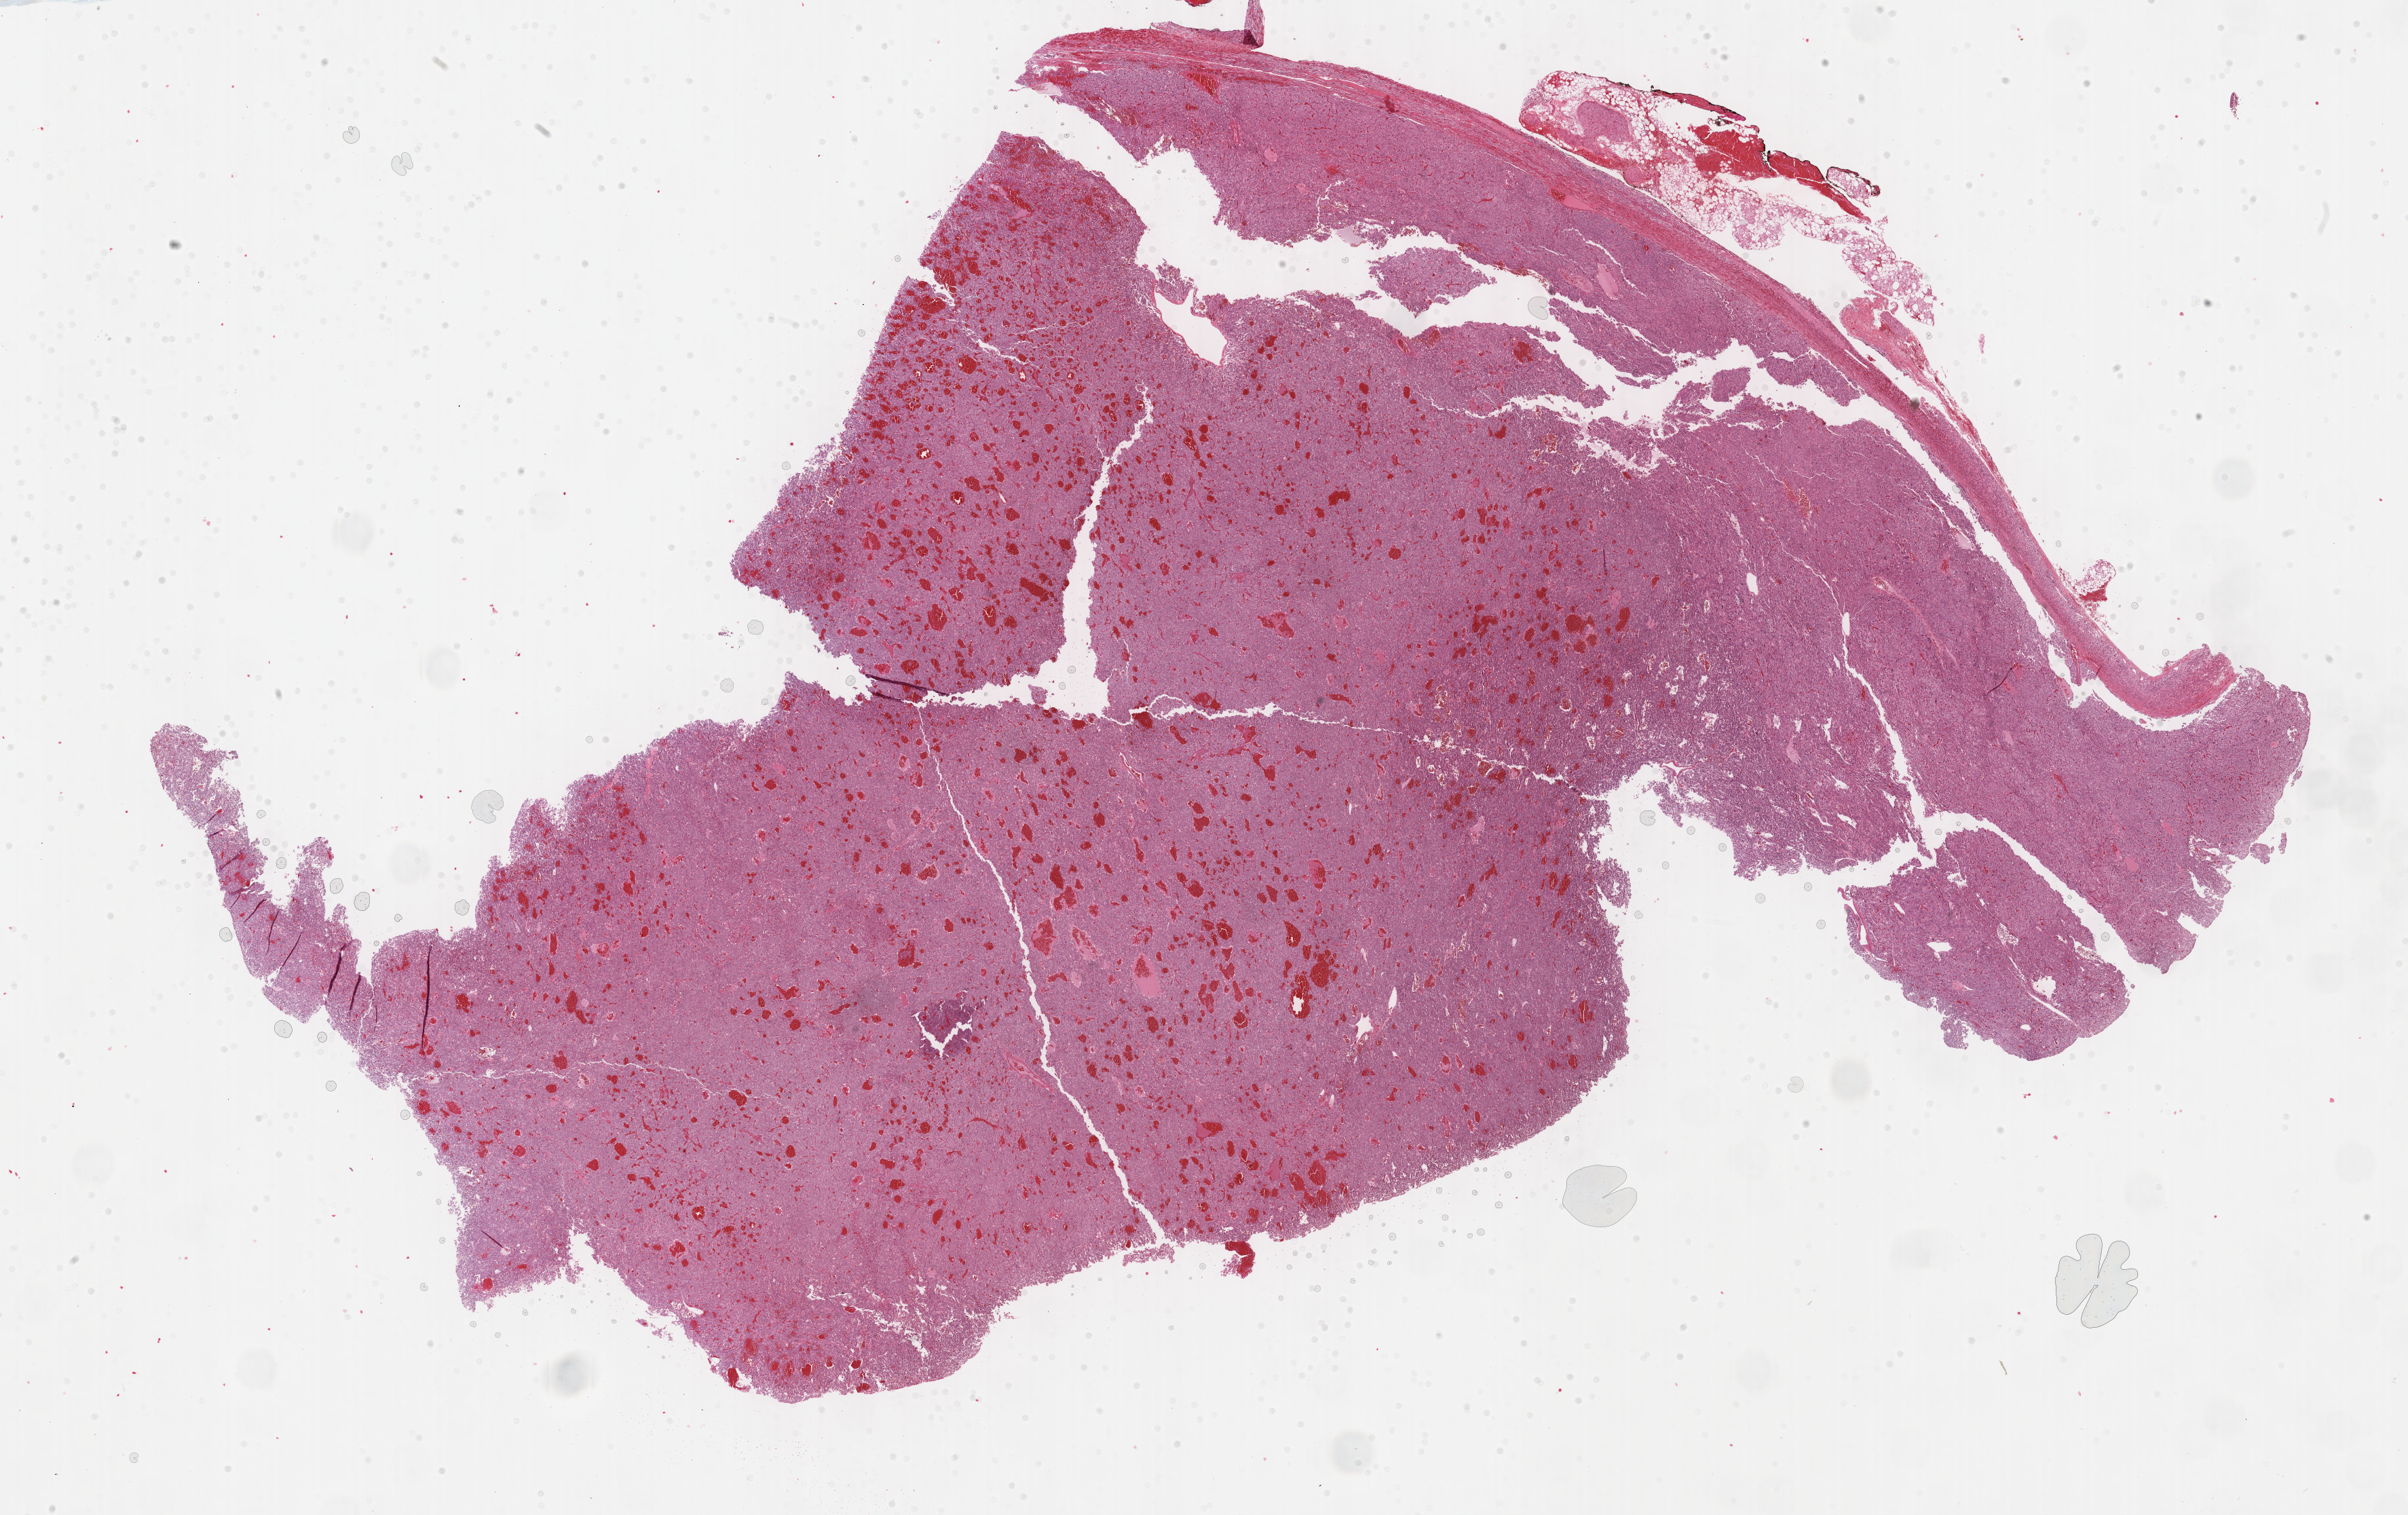
Whole-slide histology image, H&E — whole scanned area (about 28.7 x 18.0 mm) shown as a low-resolution overview; formalin-fixed paraffin-embedded (FFPE) diagnostic section; primary tumour sample from the adrenal gland. Female, age 37 years at initial diagnosis.
Diagnosis: Pheochromocytoma, NOS.